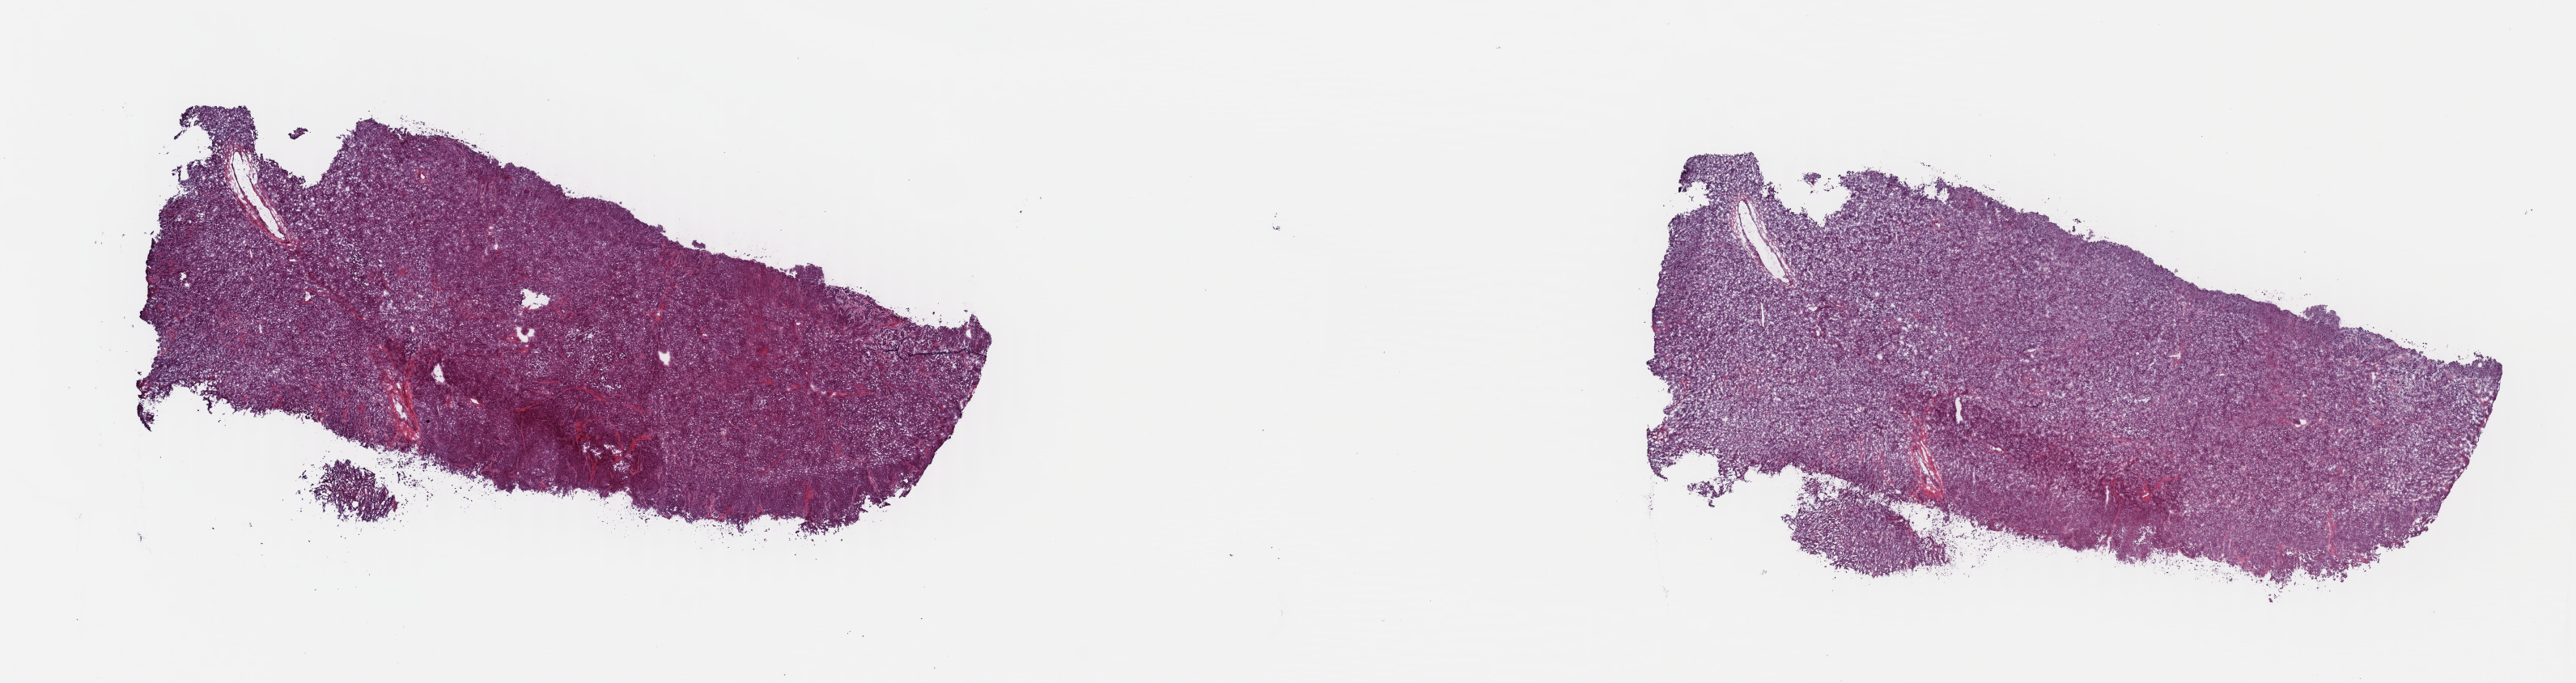
Digitized H&E-stained tissue section (whole slide), low-resolution overview of the scanned area, about 25.0 x 6.6 mm (slide scanned at 40x); frozen section from the top of the tissue portion; primary tumour sample from the adrenal cortex. Female, age 53 years at initial diagnosis. Pathologist review of this section (percent, as recorded): tumour cells 80%, tumour nuclei 95%, normal cells 0%, stromal cells 10%, necrosis 10%. Infiltration values recorded for this section: lymphocyte infiltration 0%, monocyte infiltration 0%, neutrophil infiltration 0%.
Diagnosis: Adrenal cortical carcinoma (cortex of adrenal gland). Lymph nodes positive (case pathology): 3 of 3 examined.